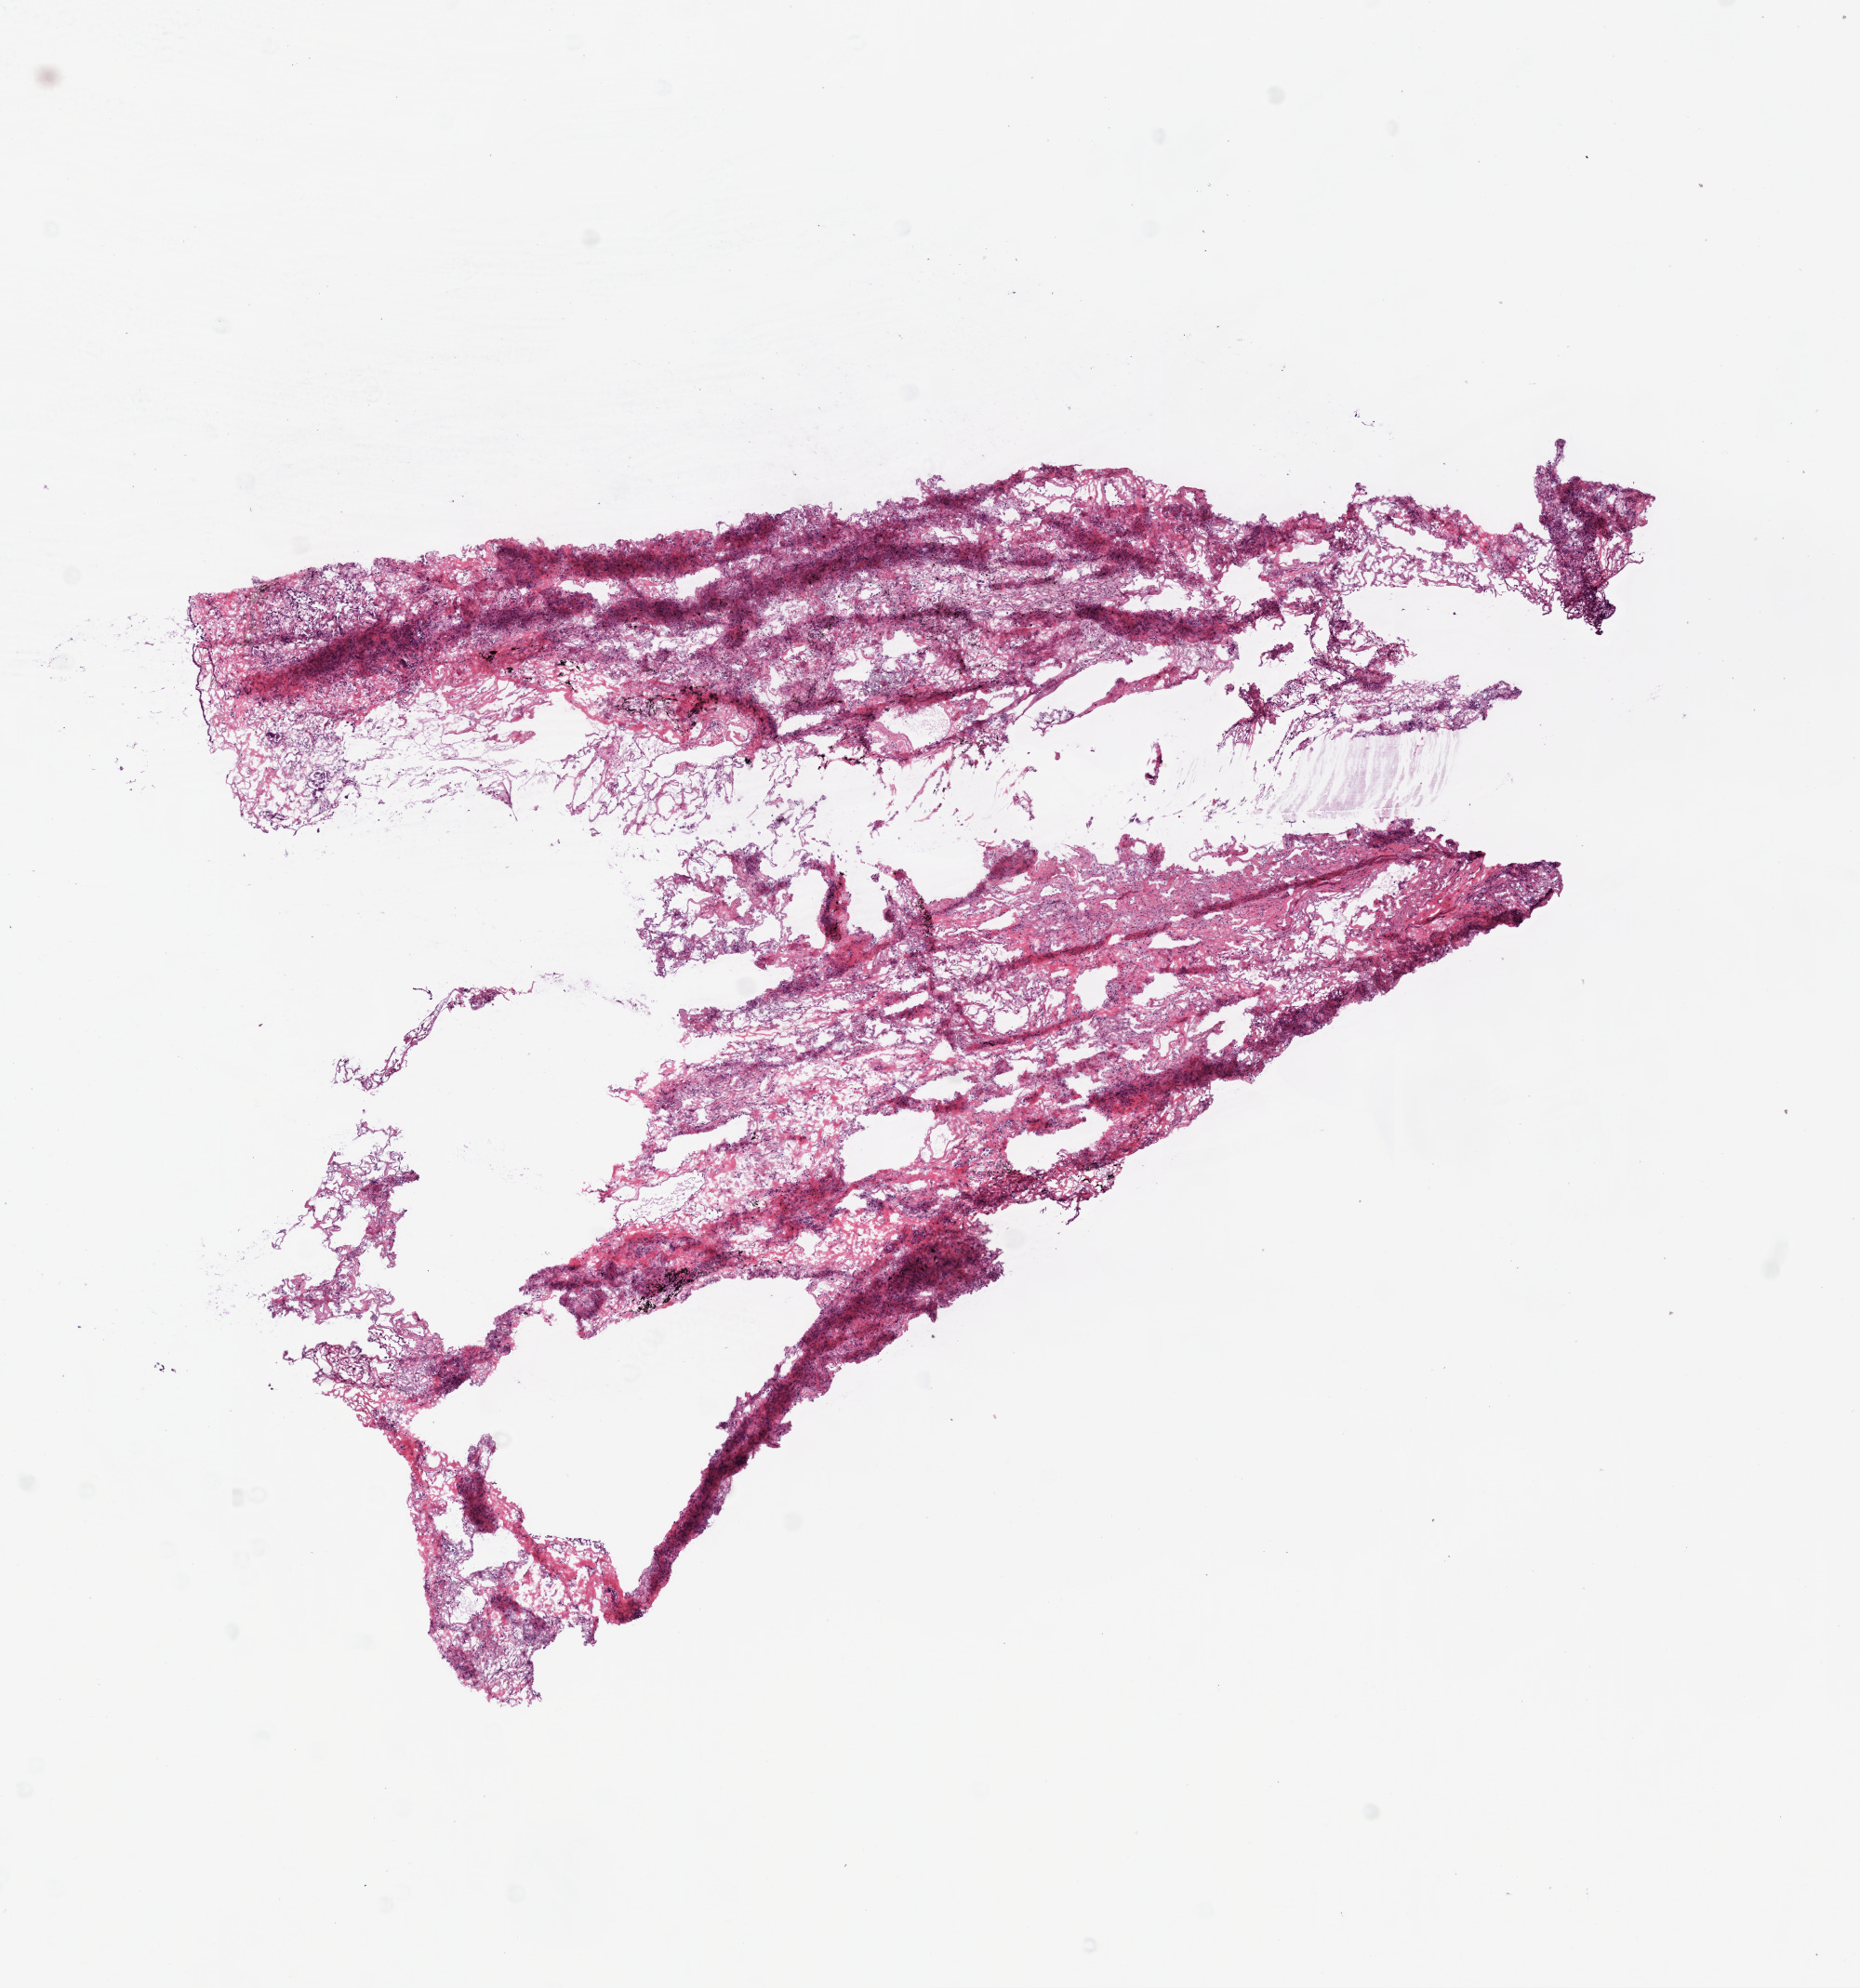
H&E-stained whole-slide image — a low-resolution overview of the entire scanned area, about 8.0 x 8.6 mm (from a 20x scan). Frozen section. Sample: solid tissue normal (non-tumour tissue), lung. Patient: female, age at initial diagnosis 62 years.
This section: solid tissue normal sample (biorepository sample class). Patient diagnosis: Squamous cell carcinoma, NOS (lower lobe, lung).